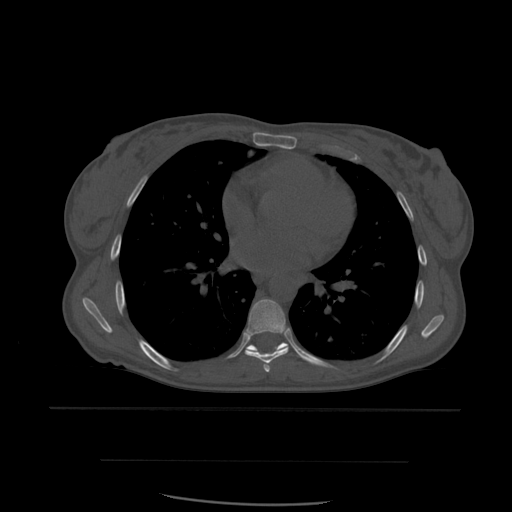
CT including the spine, one axial slice; slice 369 of 574 in the series (ordered by position); bone window (W 1800 / L 400 HU); 1.25 mm slice thickness; 512 × 512 image matrix. Patient age 48 years. From the clinical record (not read from this slice): primary cancer: lung.
Structures marked on this image (semi-automatically segmented with operator editing):
- T6 vertebra: bounding box [x1, y1, x2, y2] px = [264, 365, 270, 372]
- T7 vertebra: [245, 299, 289, 372]
- T8 vertebra: [246, 343, 289, 352]